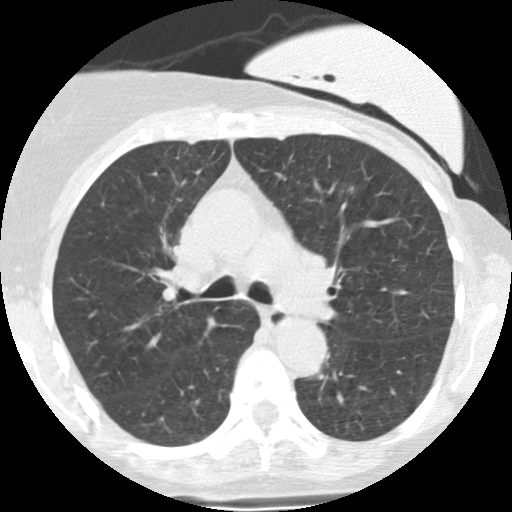
Low-dose screening chest CT, axial slice; second screening round (one year after baseline); lung window (W 1500 / L -600 HU); 2.5 mm slice thickness; standard (soft-tissue) reconstruction kernel (STANDARD); slice 91 of 251 in the series. Female participant, aged 66 years at enrolment. Former smoker at enrolment.
Lesion marked by an expert reader, box from (x=344, y=182) to (x=359, y=201) px. Screening reader's record for this exam (one nodule recorded; not confirmed to be the boxed lesion): non-calcified nodule or mass ≥4 mm, left upper lobe, 7 × 5 mm, smooth margins, soft tissue attenuation, pre-existing on the prior screen: yes; interval growth: yes. Later outcome: lung cancer diagnosed 218 days after this screen — adenocarcinoma, NOS, left lower lobe, poorly differentiated (G3), stage IA (AJCC 6th edition), 8 mm at pathology.